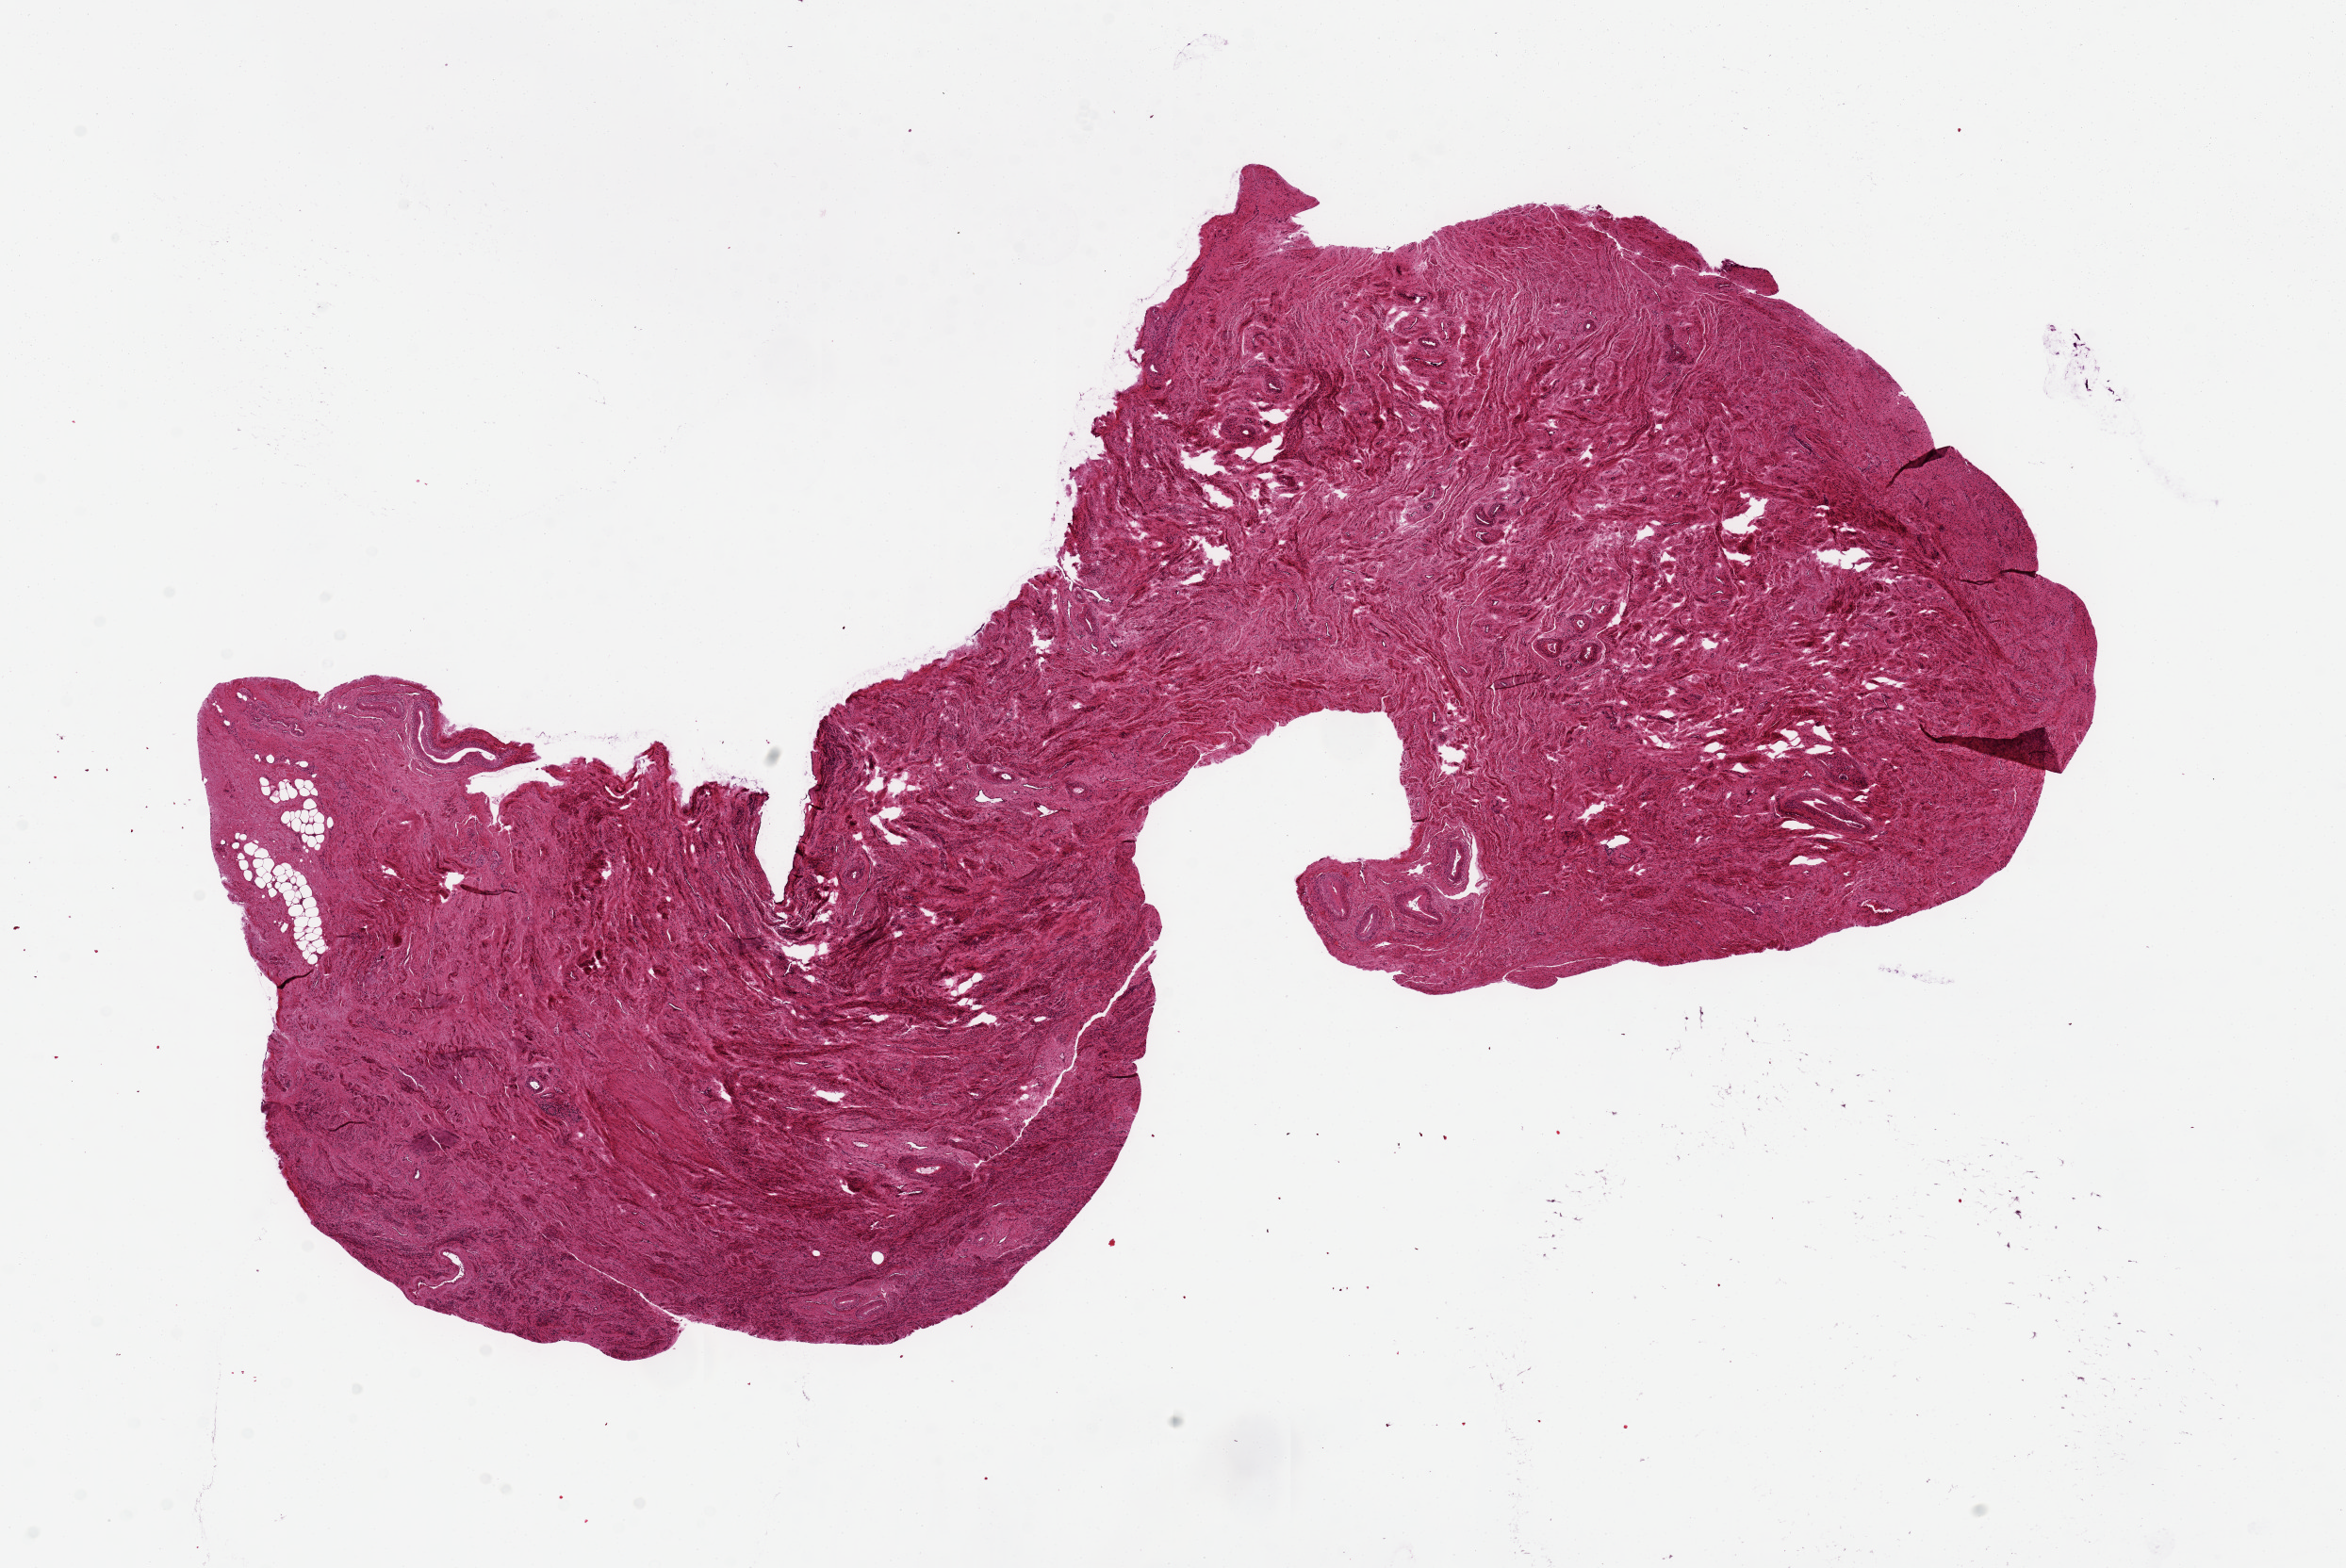
Digitized H&E-stained section, shown as a low-resolution overview of the whole scanned area (about 19.7 x 13.2 mm).
Specimen: PAXgene-fixed paraffin-embedded (PFPE) section; section of exocervix (target tissue); tissue donor sample.